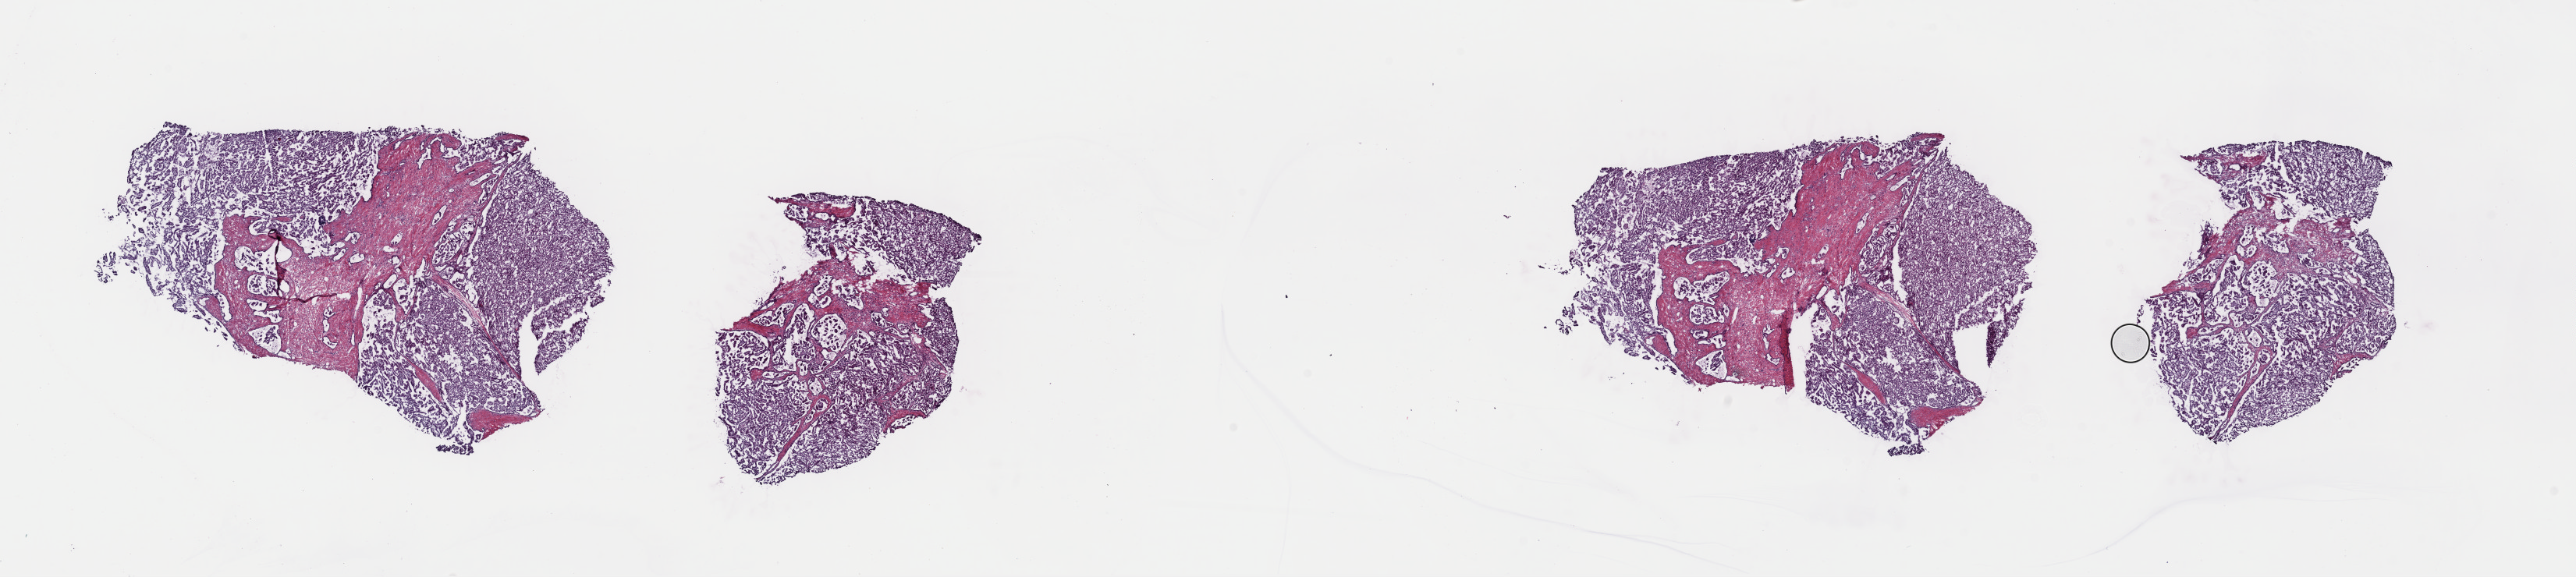
Whole-slide histology image, H&E, whole scanned area (about 26.1 x 5.8 mm, from a 40x scan) shown as a low-resolution overview; frozen section from the top of the tissue portion; kidney, primary tumour sample. Patient: male, age at initial diagnosis 40 years. Slide review estimates, as recorded: tumour cells 80%, tumour nuclei 90%.
Histologic diagnosis: Papillary adenocarcinoma, NOS.